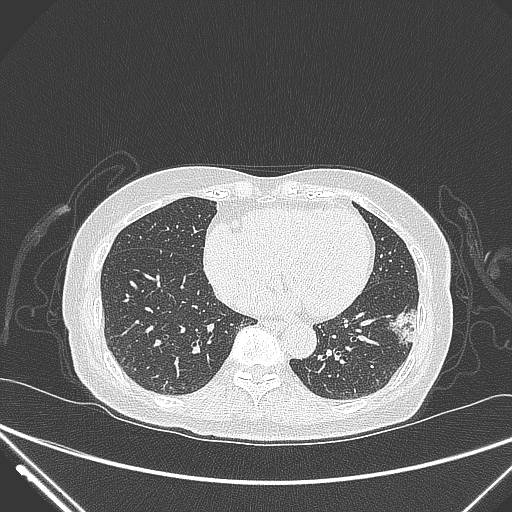
Chest CT, one axial slice; position 108 of 310 along the scan axis; lung window (W 1500 / L -600 HU); 1 mm slice thickness; 512 × 512 image matrix, field of view 377 × 377 mm. Female patient, age 82 years. From the clinical record (not read from this slice): clinical TNM (as recorded): T1c N0 M0.
Outlined on this slice (bounding box drawn by a radiologist):
- lung tumour (recorded histology: adenocarcinoma): bounding box (x1, y1, x2, y2) in pixels: (391, 305, 422, 349)